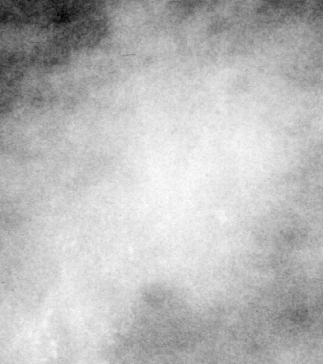
Region of interest cut from a scanned film mammogram (one marked finding), right breast, MLO view.
Mass, shape irregular / architectural distortion, margins obscured / ill defined / spiculated; BI-RADS assessment category 4; pathology (as recorded): malignant.